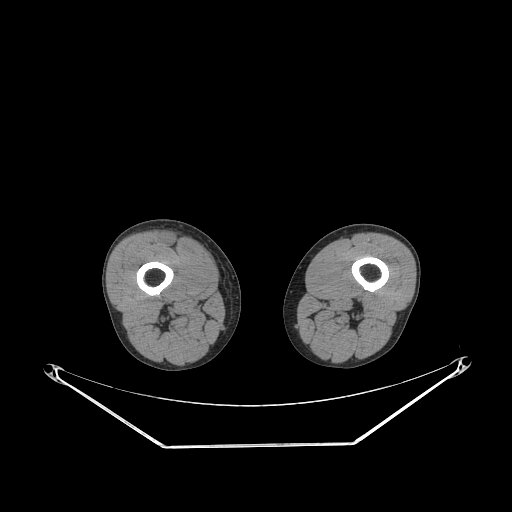
CT of an extremity soft-tissue mass (from a PET/CT study), one axial slice. Slice 224 of 311 in the series (ordered by position). Soft-tissue window (W 400 / L 40 HU). 3.75 mm slice thickness. 512 × 512 image matrix, field of view 500 × 500 mm. Male patient. Case-level facts recorded for this patient, not image findings: histological type: pleiomorphic leiomyosarcoma; grade: intermediate; site of the primary tumour: right thigh.
Annotated regions visible in this slice (expert contour drawn on MRI and transferred to this co-registered scan by the dataset authors):
- gross tumour volume including surrounding oedema: bounding box <164,235,179,245> (left, top, right, bottom; pixels)